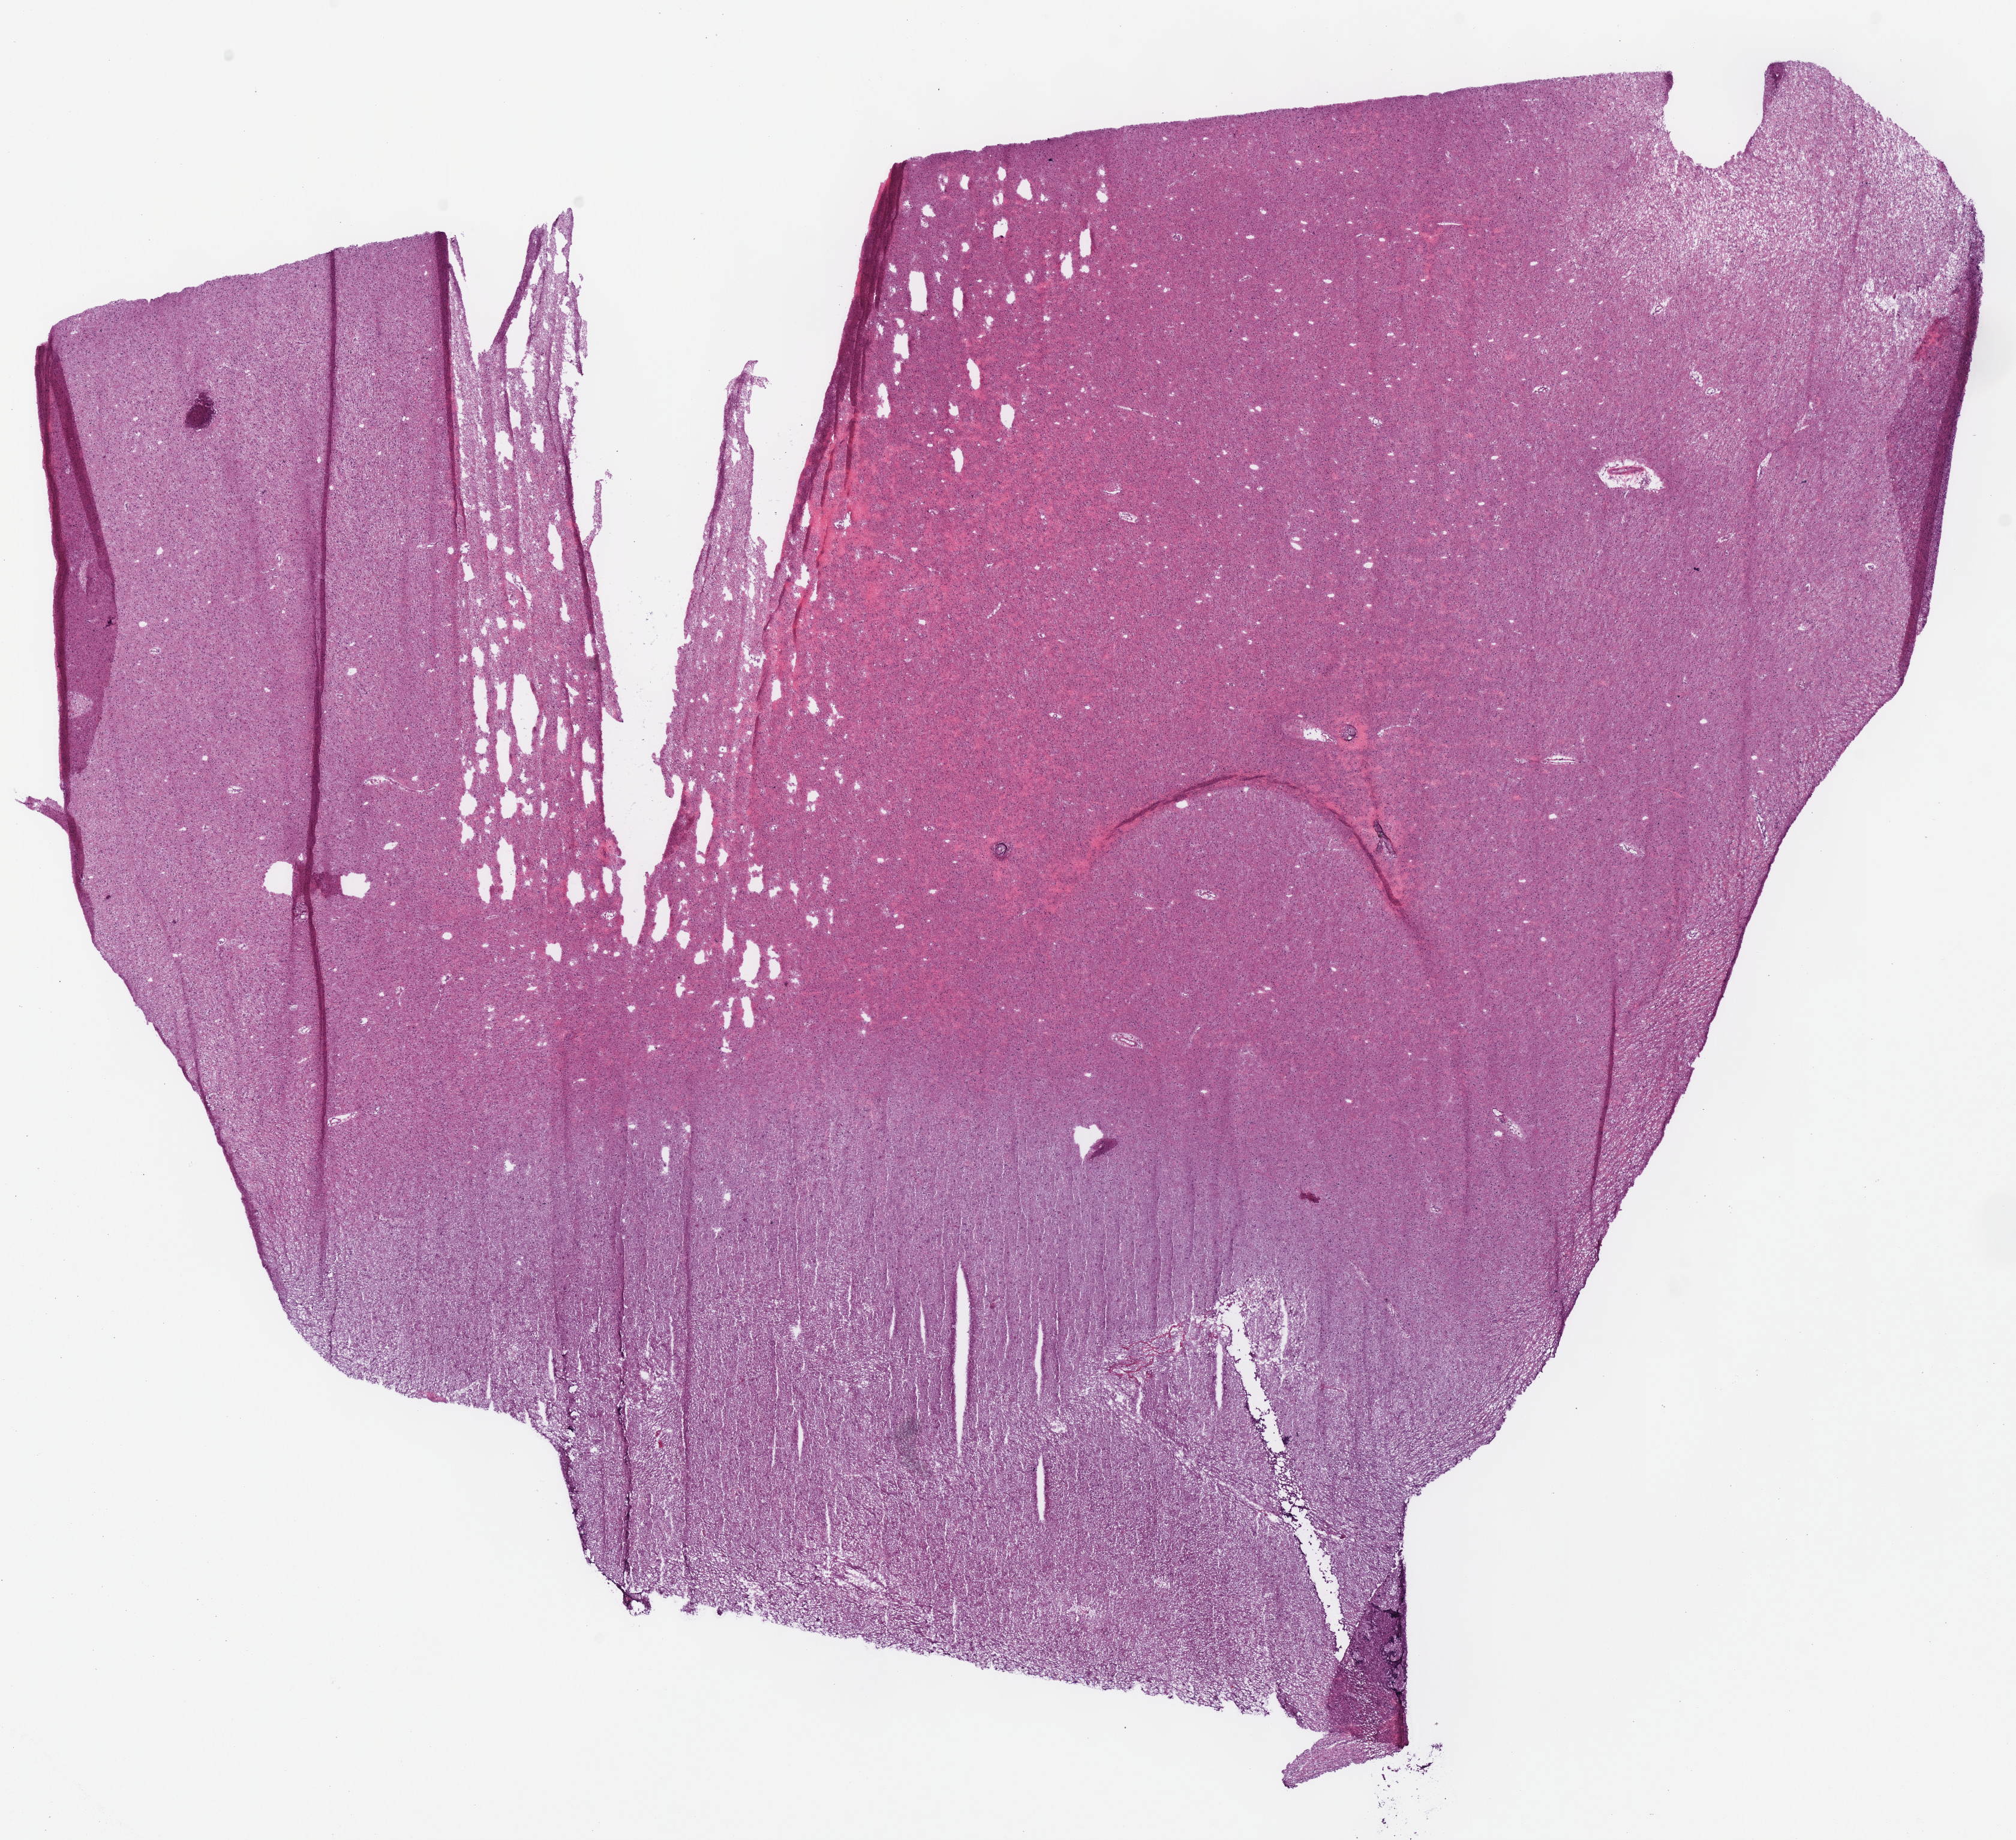
Hematoxylin and eosin (H&E) stained whole-slide image — shown as a low-resolution overview of the whole scanned area (about 13.2 x 12.1 mm, acquisition: 40x scan), frozen section, primary tumour sample from the brain. Patient: male, age at initial diagnosis 31 years. Histologic grade: G2 (moderately differentiated). Slide review estimates, as recorded: tumour cells 100%, tumour nuclei 65%, normal cells 0%, stromal cells 0%, necrosis 0%.
Histologic diagnosis: Mixed glioma (cerebrum).